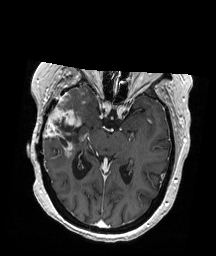
Brain MRI from a brain-tumour surgery series, one axial slice; slice 113 of 192 in the series (ordered by position); T1-weighted post-contrast; 216 × 256 image matrix. Case-level facts recorded for this patient, not image findings: histopathology: Glioblastoma; WHO grade: 4; IDH mutation: no.
Annotated regions visible in this slice (outlined manually by an expert reader):
- tumour: bounding box (x1, y1, x2, y2) in pixels: (43, 94, 85, 158)